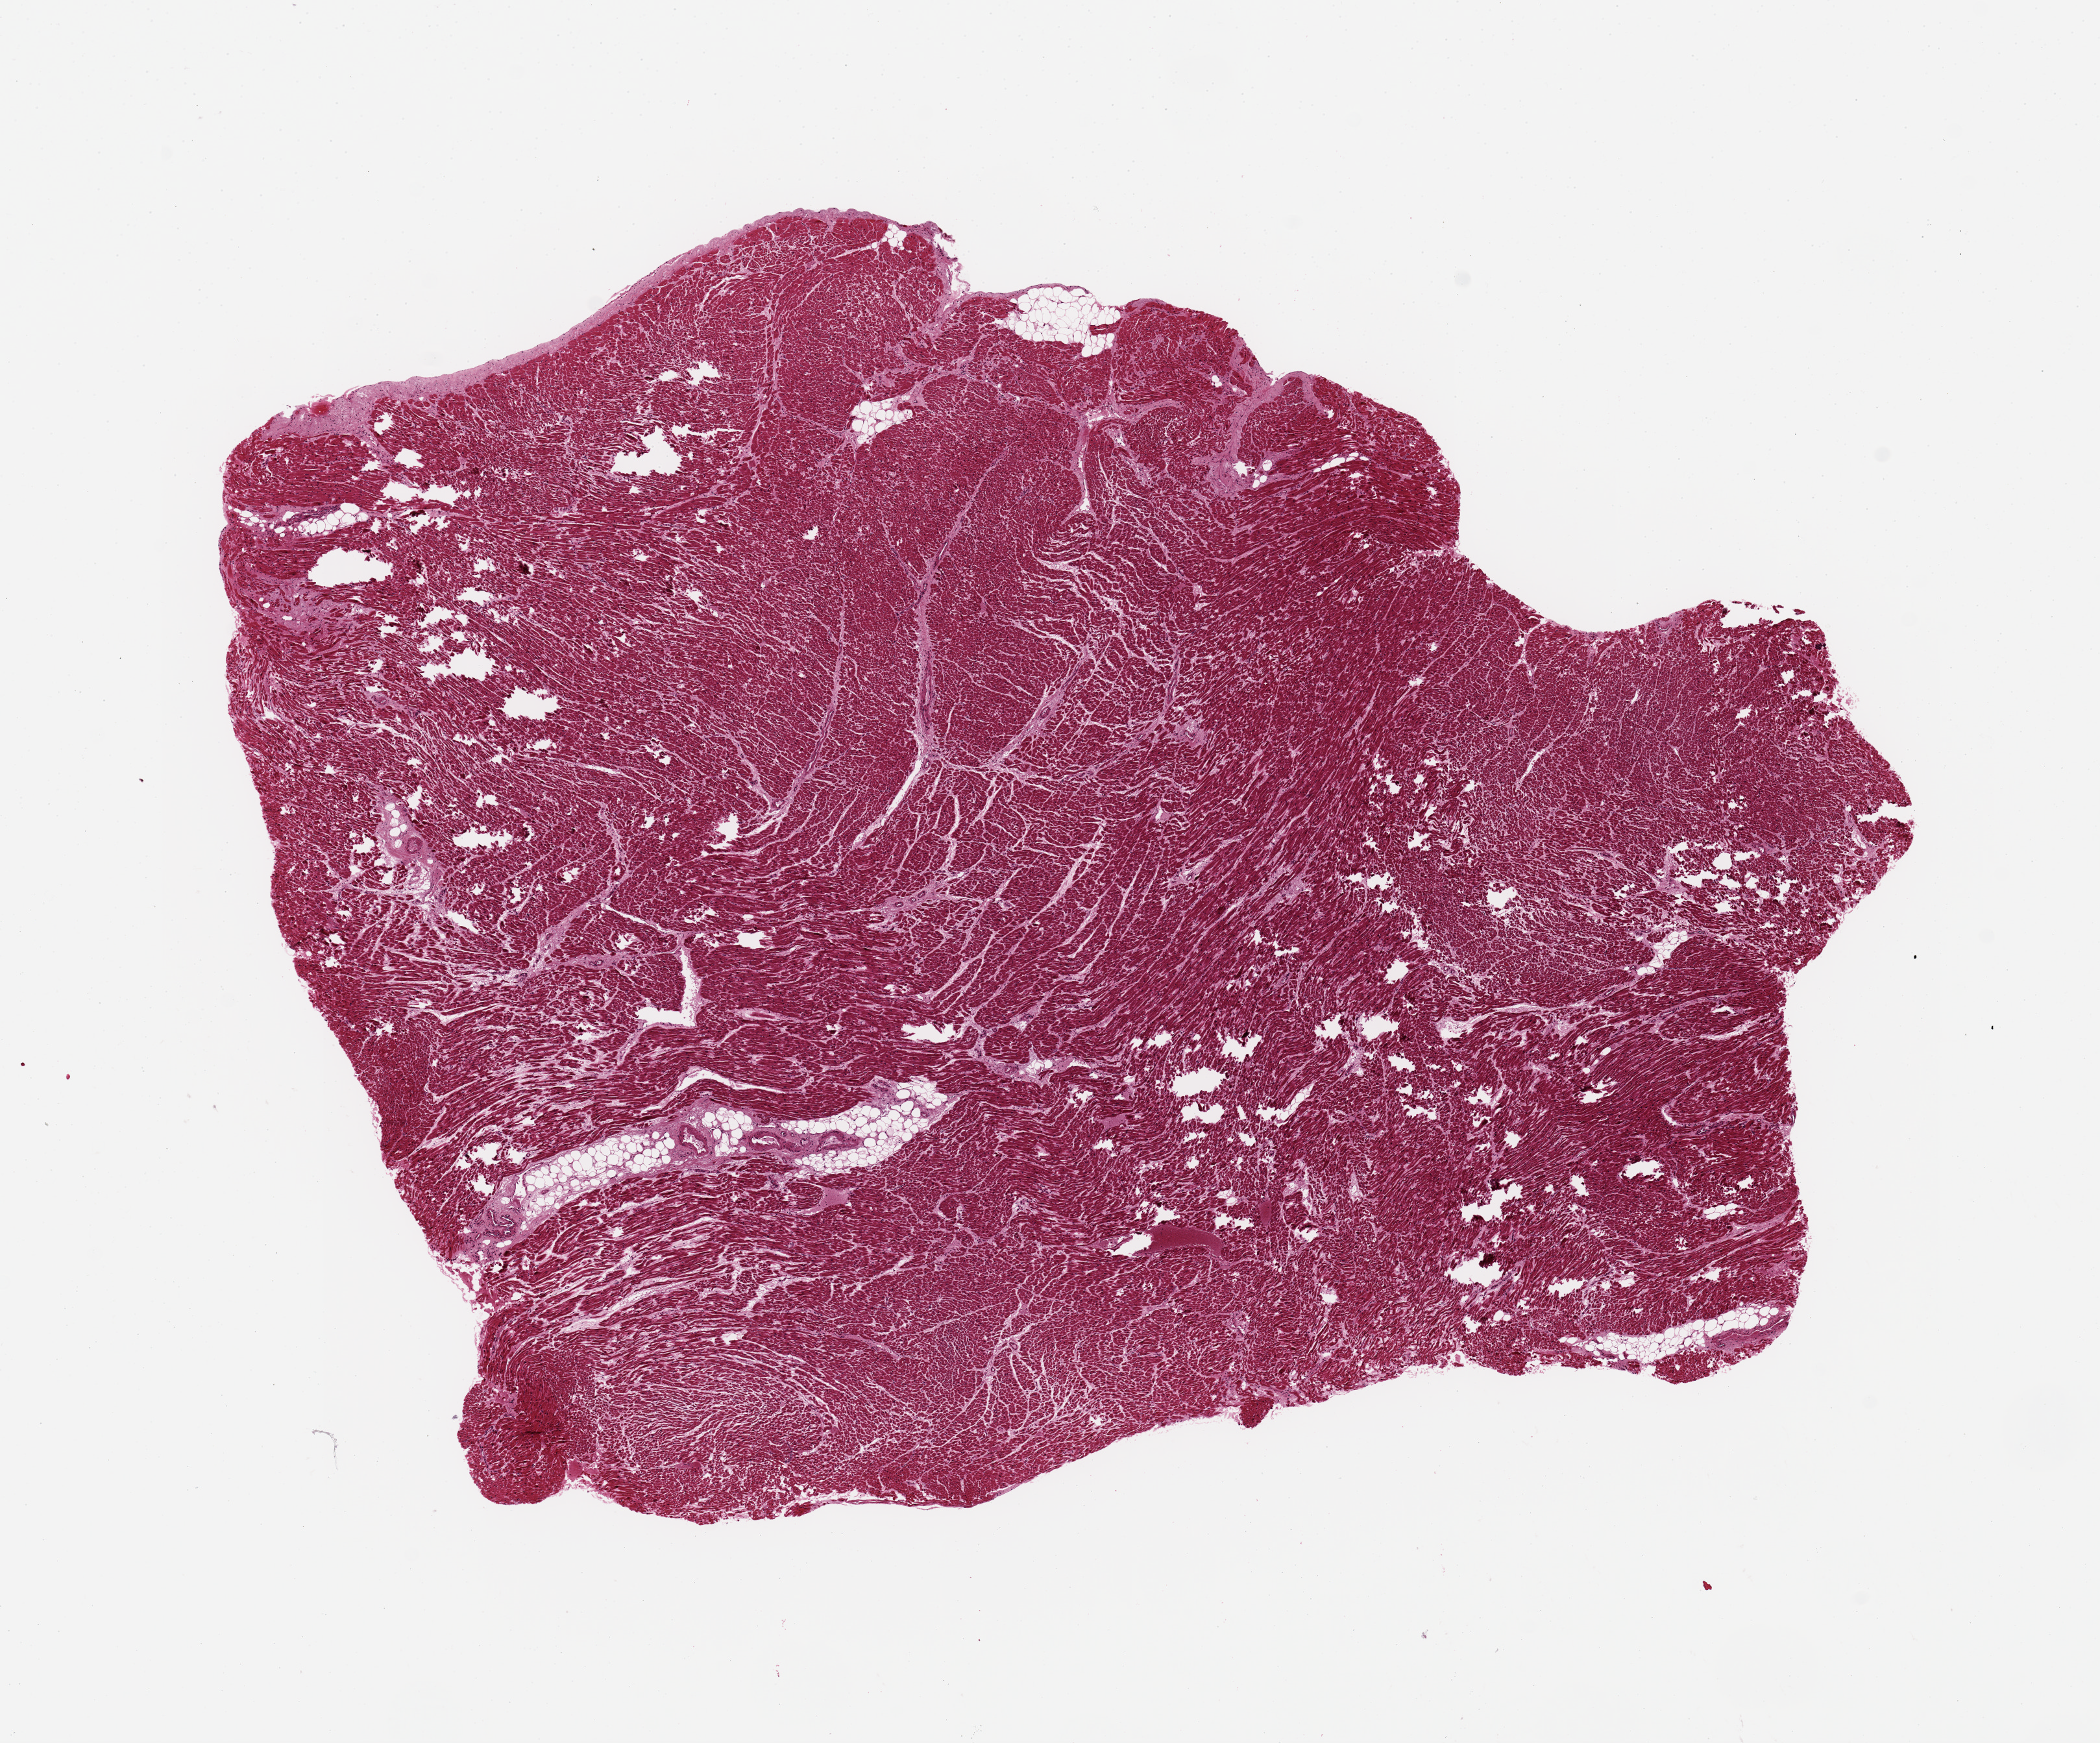
Whole-slide image, haematoxylin and eosin stain, brightfield — whole scanned area (about 12.8 x 10.6 mm) shown as a low-resolution overview; PAXgene-fixed paraffin-embedded (PFPE) section; target tissue: heart; donor tissue sample. Female donor.
Reviewer comment on this tissue sample: 7.8x7.5mm. Under-fixed with holes/tears. Mild ischemic changes.